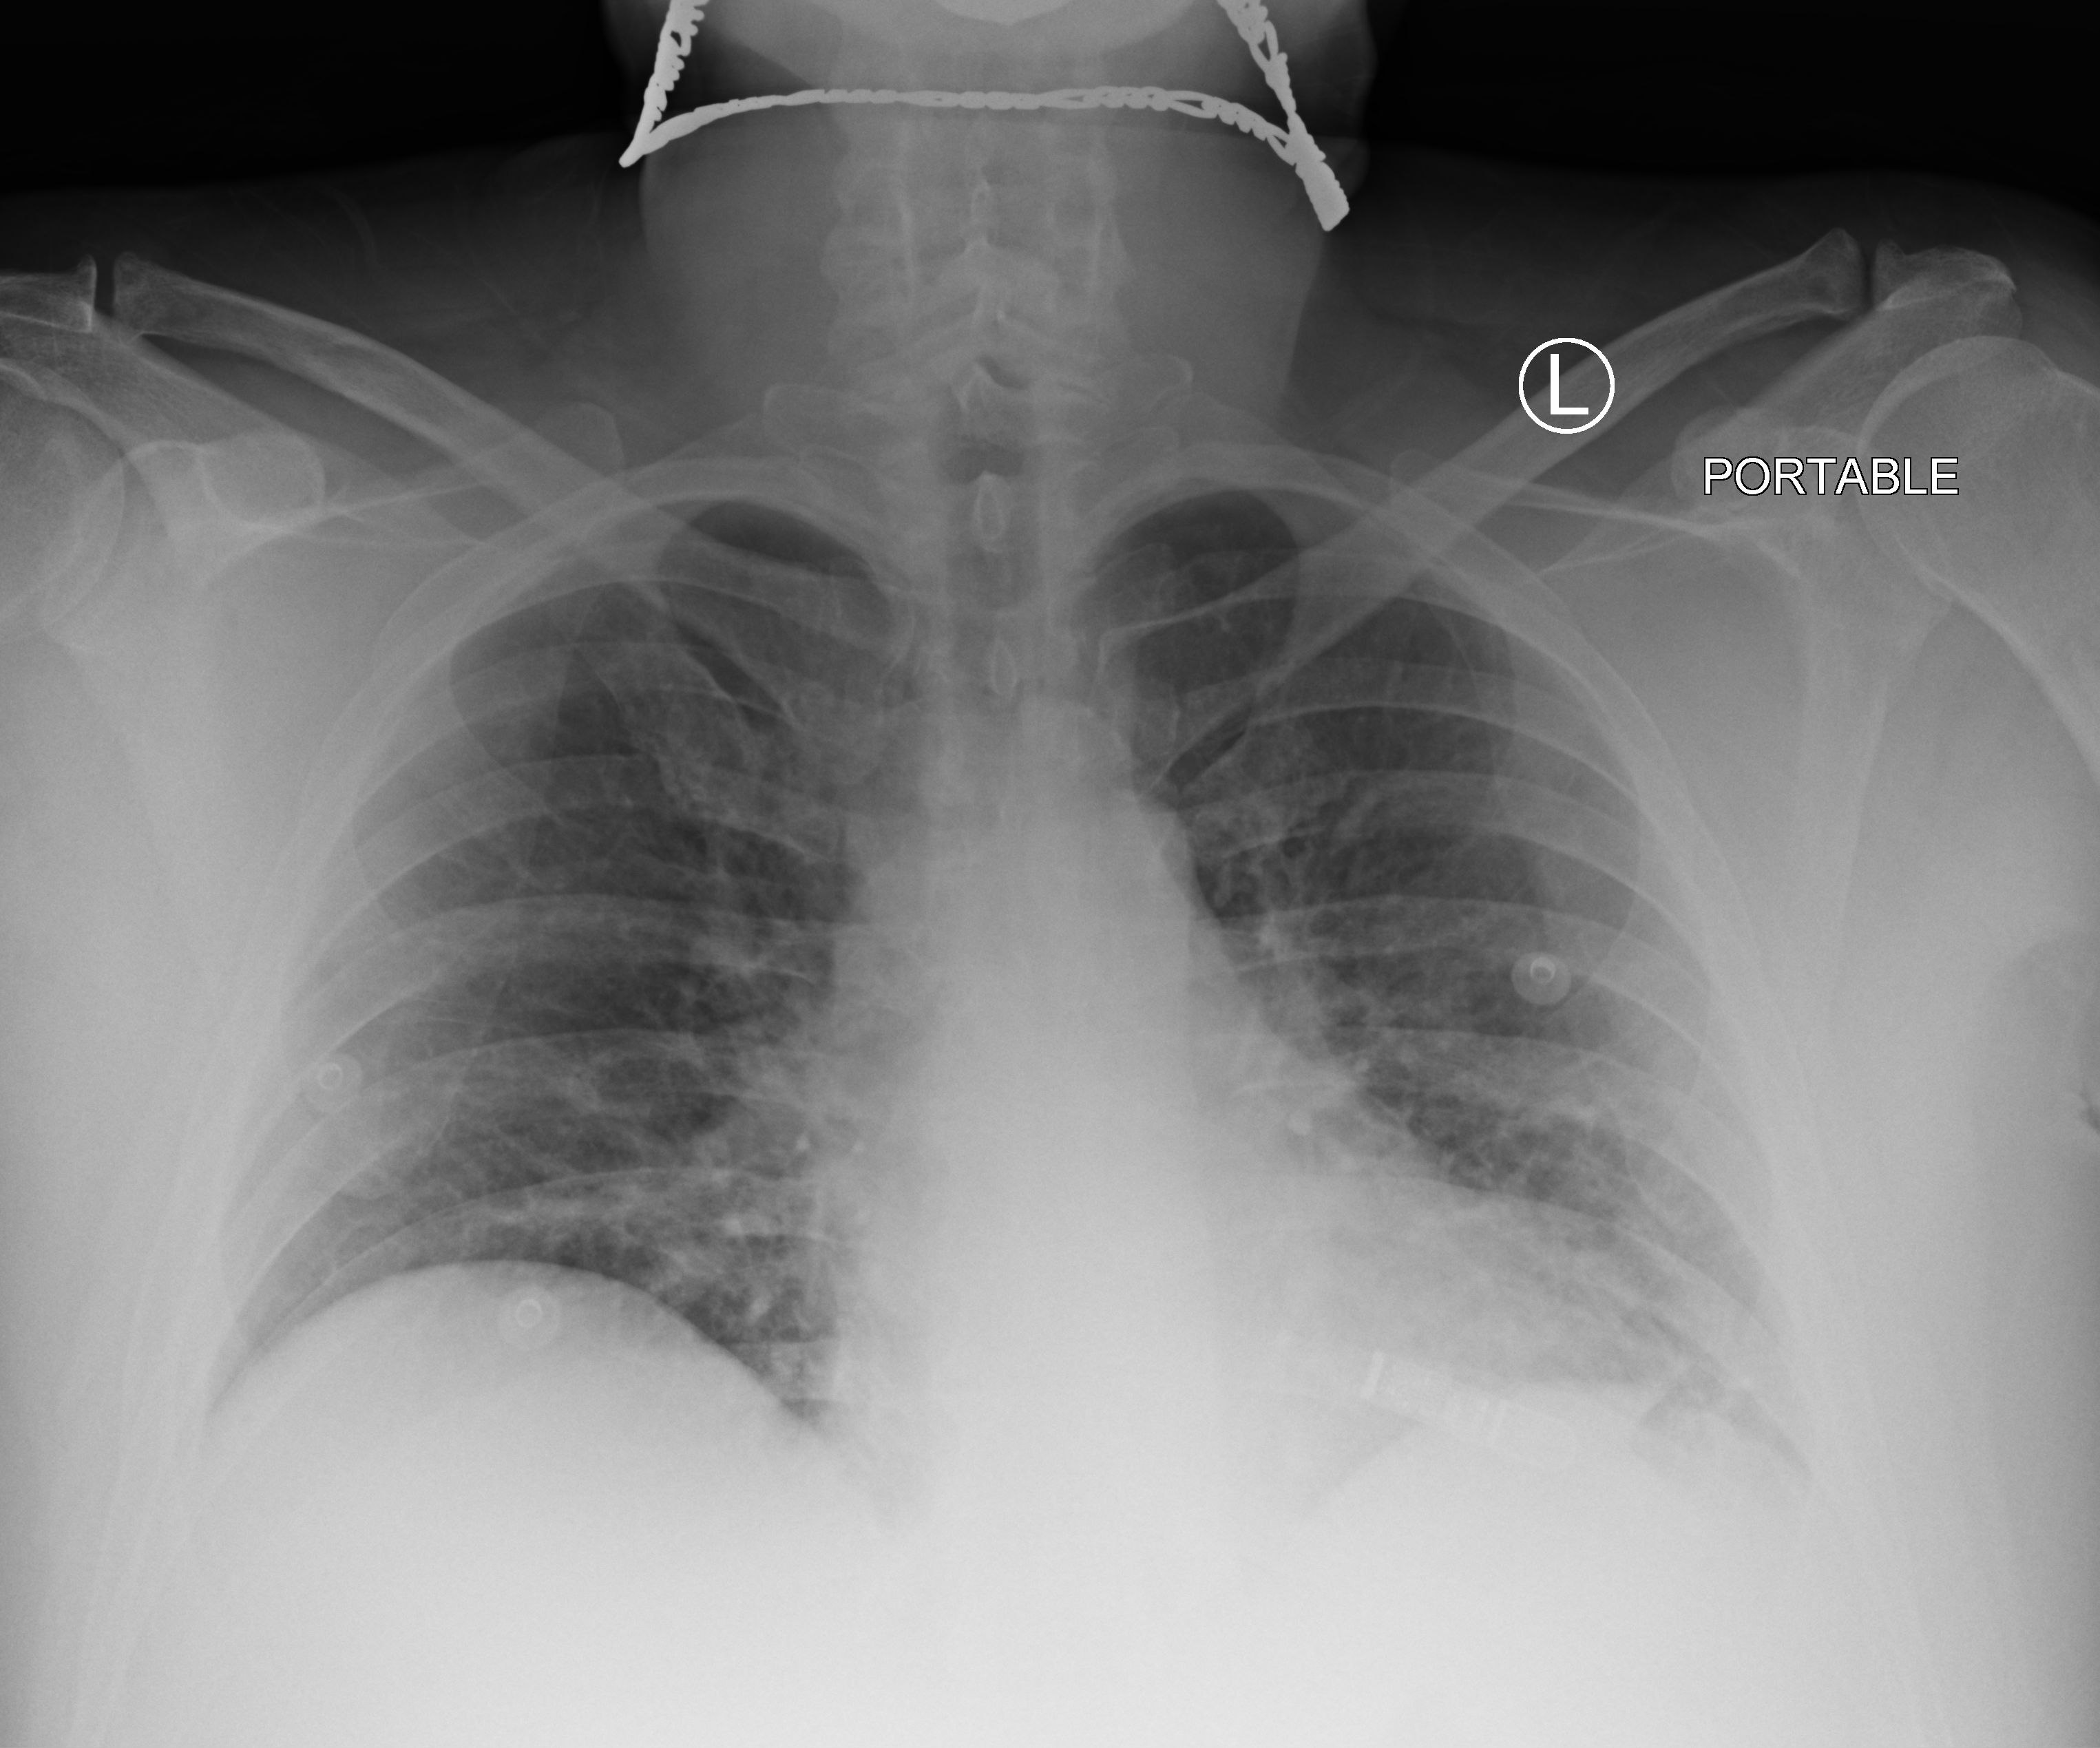
Bedside chest radiograph (computed radiography), anteroposterior (AP) projection. Patient hospitalised with COVID-19; male, aged 18–59 years.
Admission-level facts for this patient (not findings on this image; timing relative to this image not recorded): COPD (admission record): no; admitted to intensive care during this hospital stay: yes.